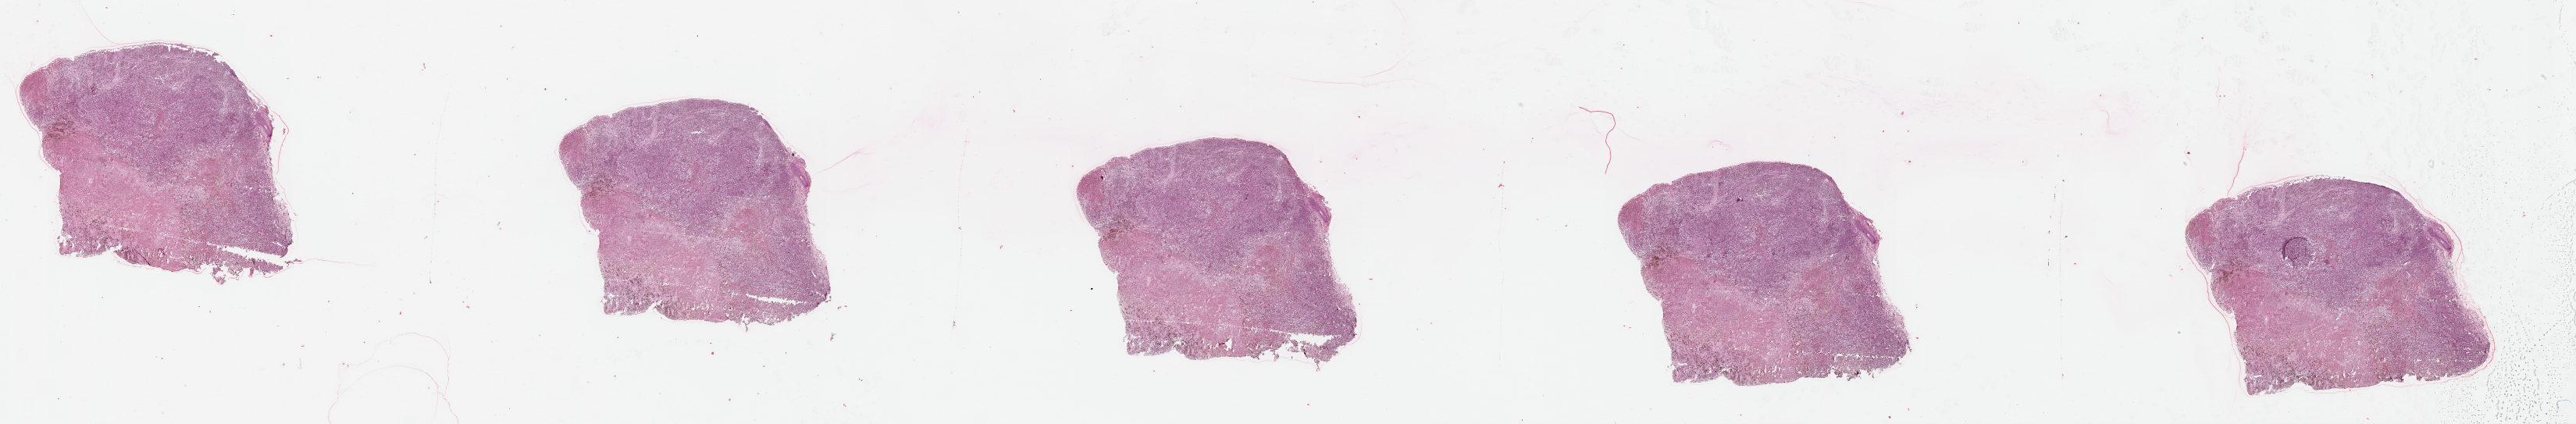
H&E whole-slide image — shown as a low-resolution overview of the whole scanned area (about 53.1 x 8.7 mm, slide scanned at 20x). Patient: female, age 76 years.
- patient diagnosis: Malignant melanoma, NOS